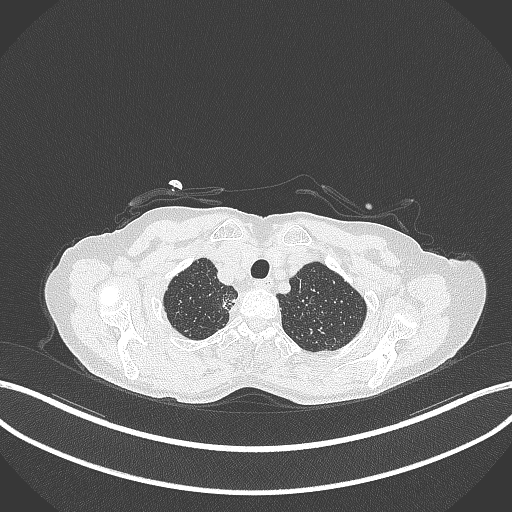
Chest CT, one axial slice; slice 334 of 403 in the series (ordered by position); lung window (W 1500 / L -600 HU); 1 mm slice thickness; 512 × 512 image matrix, field of view 400 × 400 mm. Patient: female, 75 years. Case-level facts recorded for this patient, not image findings: clinical TNM (as recorded): T1c N1 M1.
Outlined on this slice (rectangle marked by the reading radiologist):
- lung tumour (recorded histology: adenocarcinoma): bounding box (x1, y1, x2, y2) in pixels: (217, 285, 242, 314)